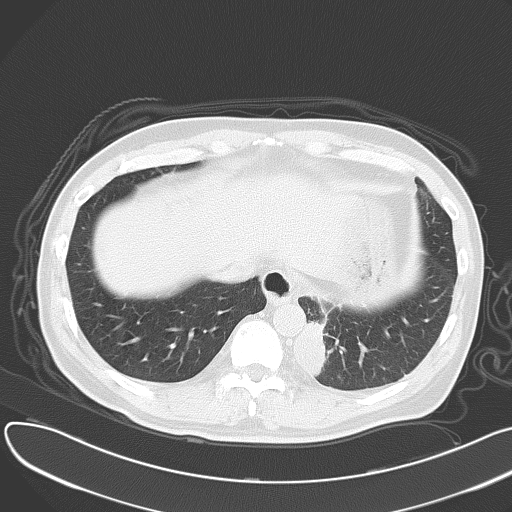
Chest CT, one axial slice; position 11 of 55 along the scan axis; 120 kVp; lung window (W 1500 / L -600 HU); 5 mm slice thickness; 512 × 512 image matrix. Male patient, age 55 years. From the clinical record (not read from this slice): clinical TNM (as recorded): T2 N3 M0.
Annotated regions visible in this slice (rectangle marked by the reading radiologist):
- lung tumour (recorded histology: small cell carcinoma): bounding box [x1, y1, x2, y2] px = [292, 320, 334, 386]